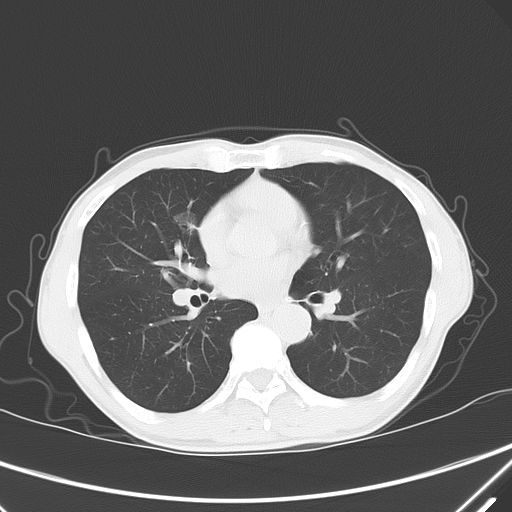
Chest CT, one axial slice; slice 34 of 68 in the series (ordered by position); 120 kVp; lung window (W 1500 / L -600 HU); 512 × 512 image matrix. Patient: male, 67 years. Case-level facts recorded for this patient, not image findings: clinical TNM (as recorded): T1c N0 M0; histopathological grade: G1-2.
Outlined on this slice (bounding box drawn by a radiologist):
- lung tumour (recorded histology: adenocarcinoma): box from (x=172, y=205) to (x=201, y=245) px